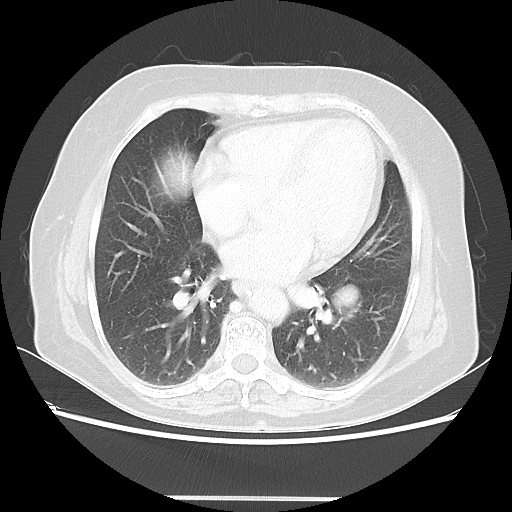
Chest CT, one axial slice; slice 25 of 56 in the series (ordered by position); reconstruction kernel LUNG; lung window (W 1500 / L -600 HU); 512 × 512 image matrix, field of view 360 × 360 mm. Patient: female, 73 years. Case-level facts recorded for this patient, not image findings: clinical TNM (as recorded): T1c N0 M0.
Outlined on this slice (rectangle marked by the reading radiologist):
- lung tumour (recorded histology: adenocarcinoma): bounding box <325,277,364,327> (left, top, right, bottom; pixels)